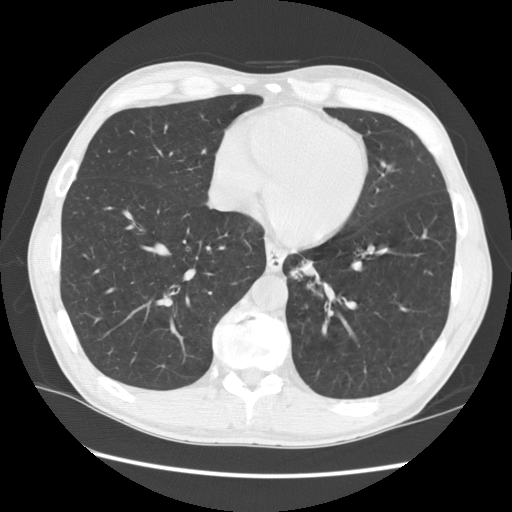
Axial slice from a low-dose chest CT screening exam, first (baseline) screen, lung window (W 1500 / L -600 HU), standard (soft-tissue) reconstruction kernel (STANDARD), 512 × 512 image matrix, field of view 360 × 360 mm. Male, age 57 years at enrolment. Current smoker at enrolment.
Expert reader's lesion annotation, bounding box (x1, y1, x2, y2) in pixels: (269, 243, 339, 306). The screening reader recorded 2 non-calcified nodules or masses ≥4 mm on this exam (left lower lobe, lingula); which of them this box marks is not recorded. Official screen result: positive, change unspecified: nodule(s) >= 4 mm or enlarging nodule(s), mass(es), or other non-specific abnormalities suspicious for lung cancer. Later outcome: lung cancer diagnosed 95 days after this screen — squamous cell carcinoma, NOS, left lower lobe, moderately differentiated (G2), stage IB (AJCC 6th edition), 35 mm at pathology.